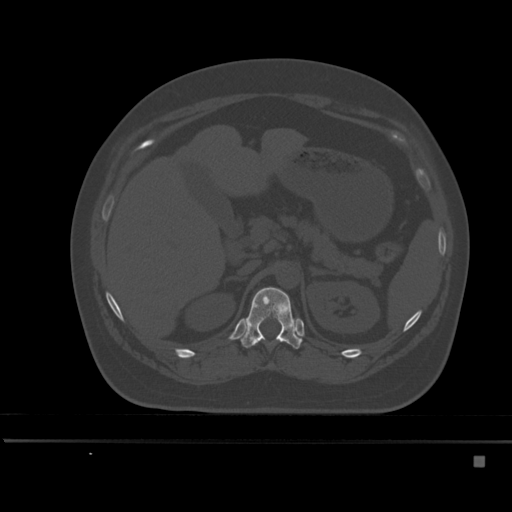
CT including the spine, one axial slice; slice 216 of 495 in the series (ordered by position); bone window (W 1800 / L 400 HU); 1.5 mm slice thickness; 512 × 512 image matrix, field of view 404 × 404 mm. Female patient, age 33 years. From the clinical record (not read from this slice): primary cancer: breast; vertebrae with lytic lesions (as recorded): T1.
Outlined on this slice (semi-automatically segmented with operator editing):
- T12 vertebra: bounding box <239,287,302,349> (left, top, right, bottom; pixels)